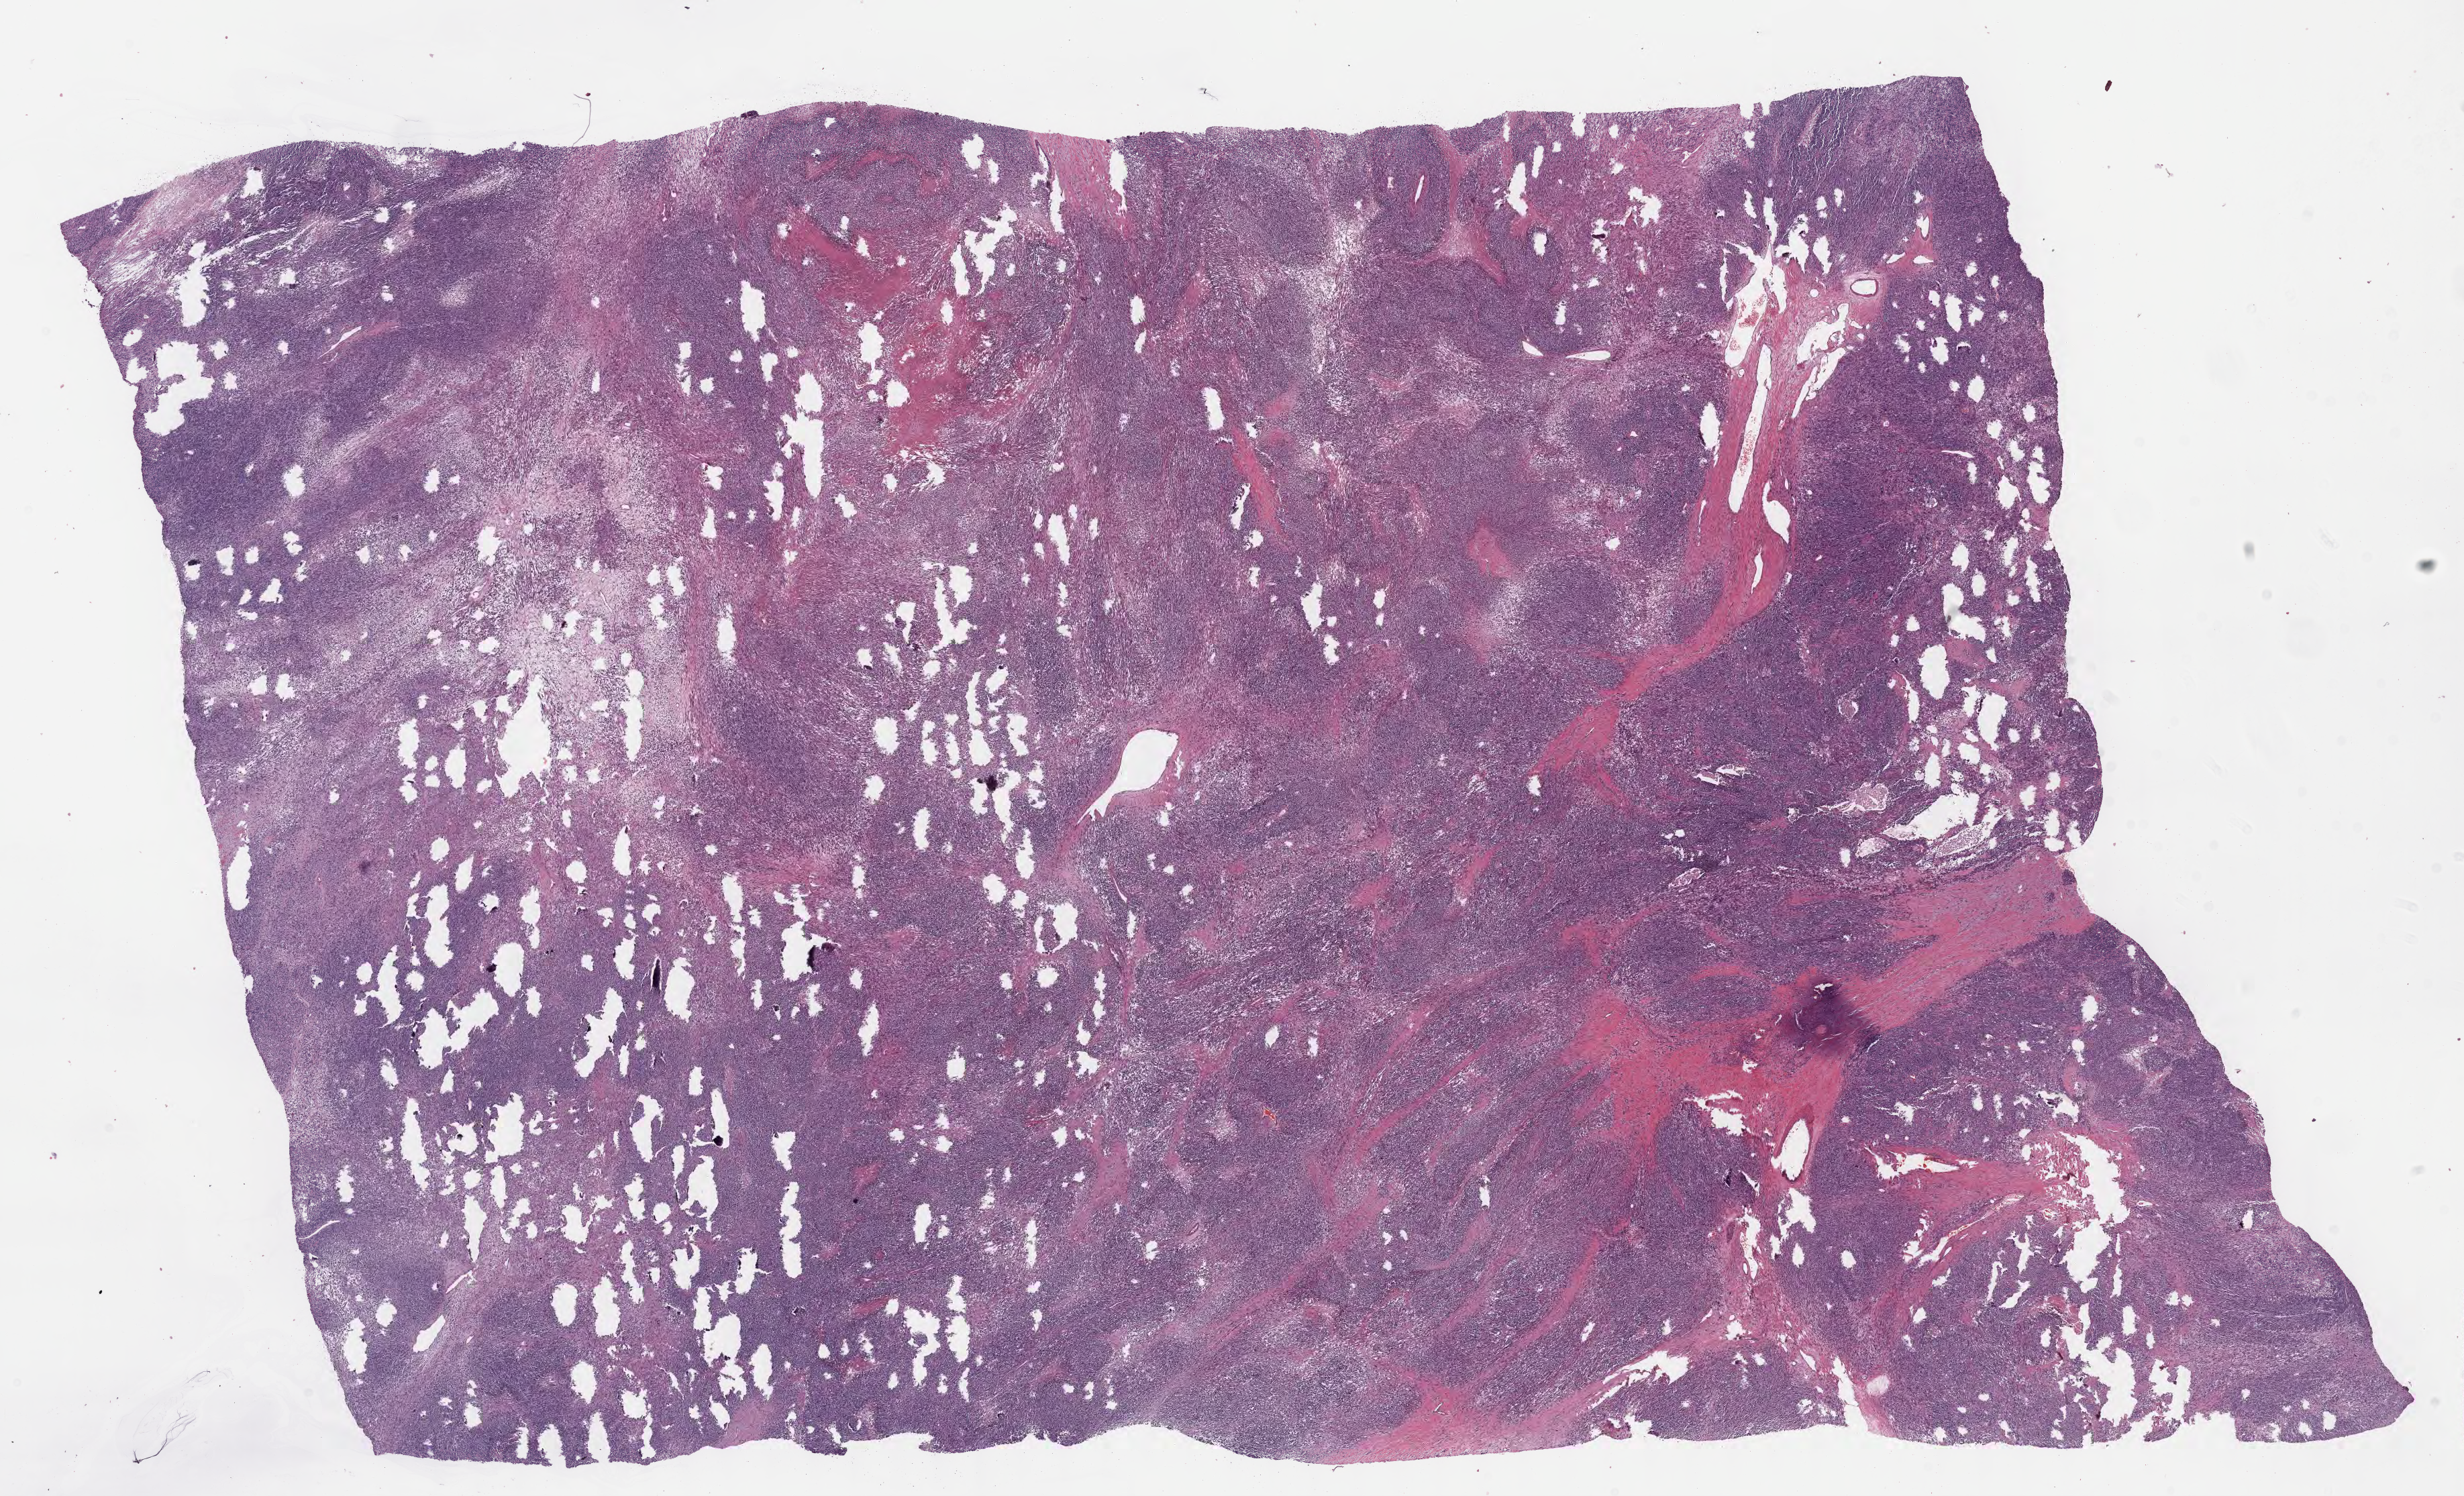
Haematoxylin and eosin whole-slide image of tumor tissue from the testis, shown as a low-resolution overview of the whole scanned area (about 29.7 x 18.0 mm); FFPE section. Patient male; age 195 months.
Recorded diagnosis: Rhabdomyosarcoma, NOS.